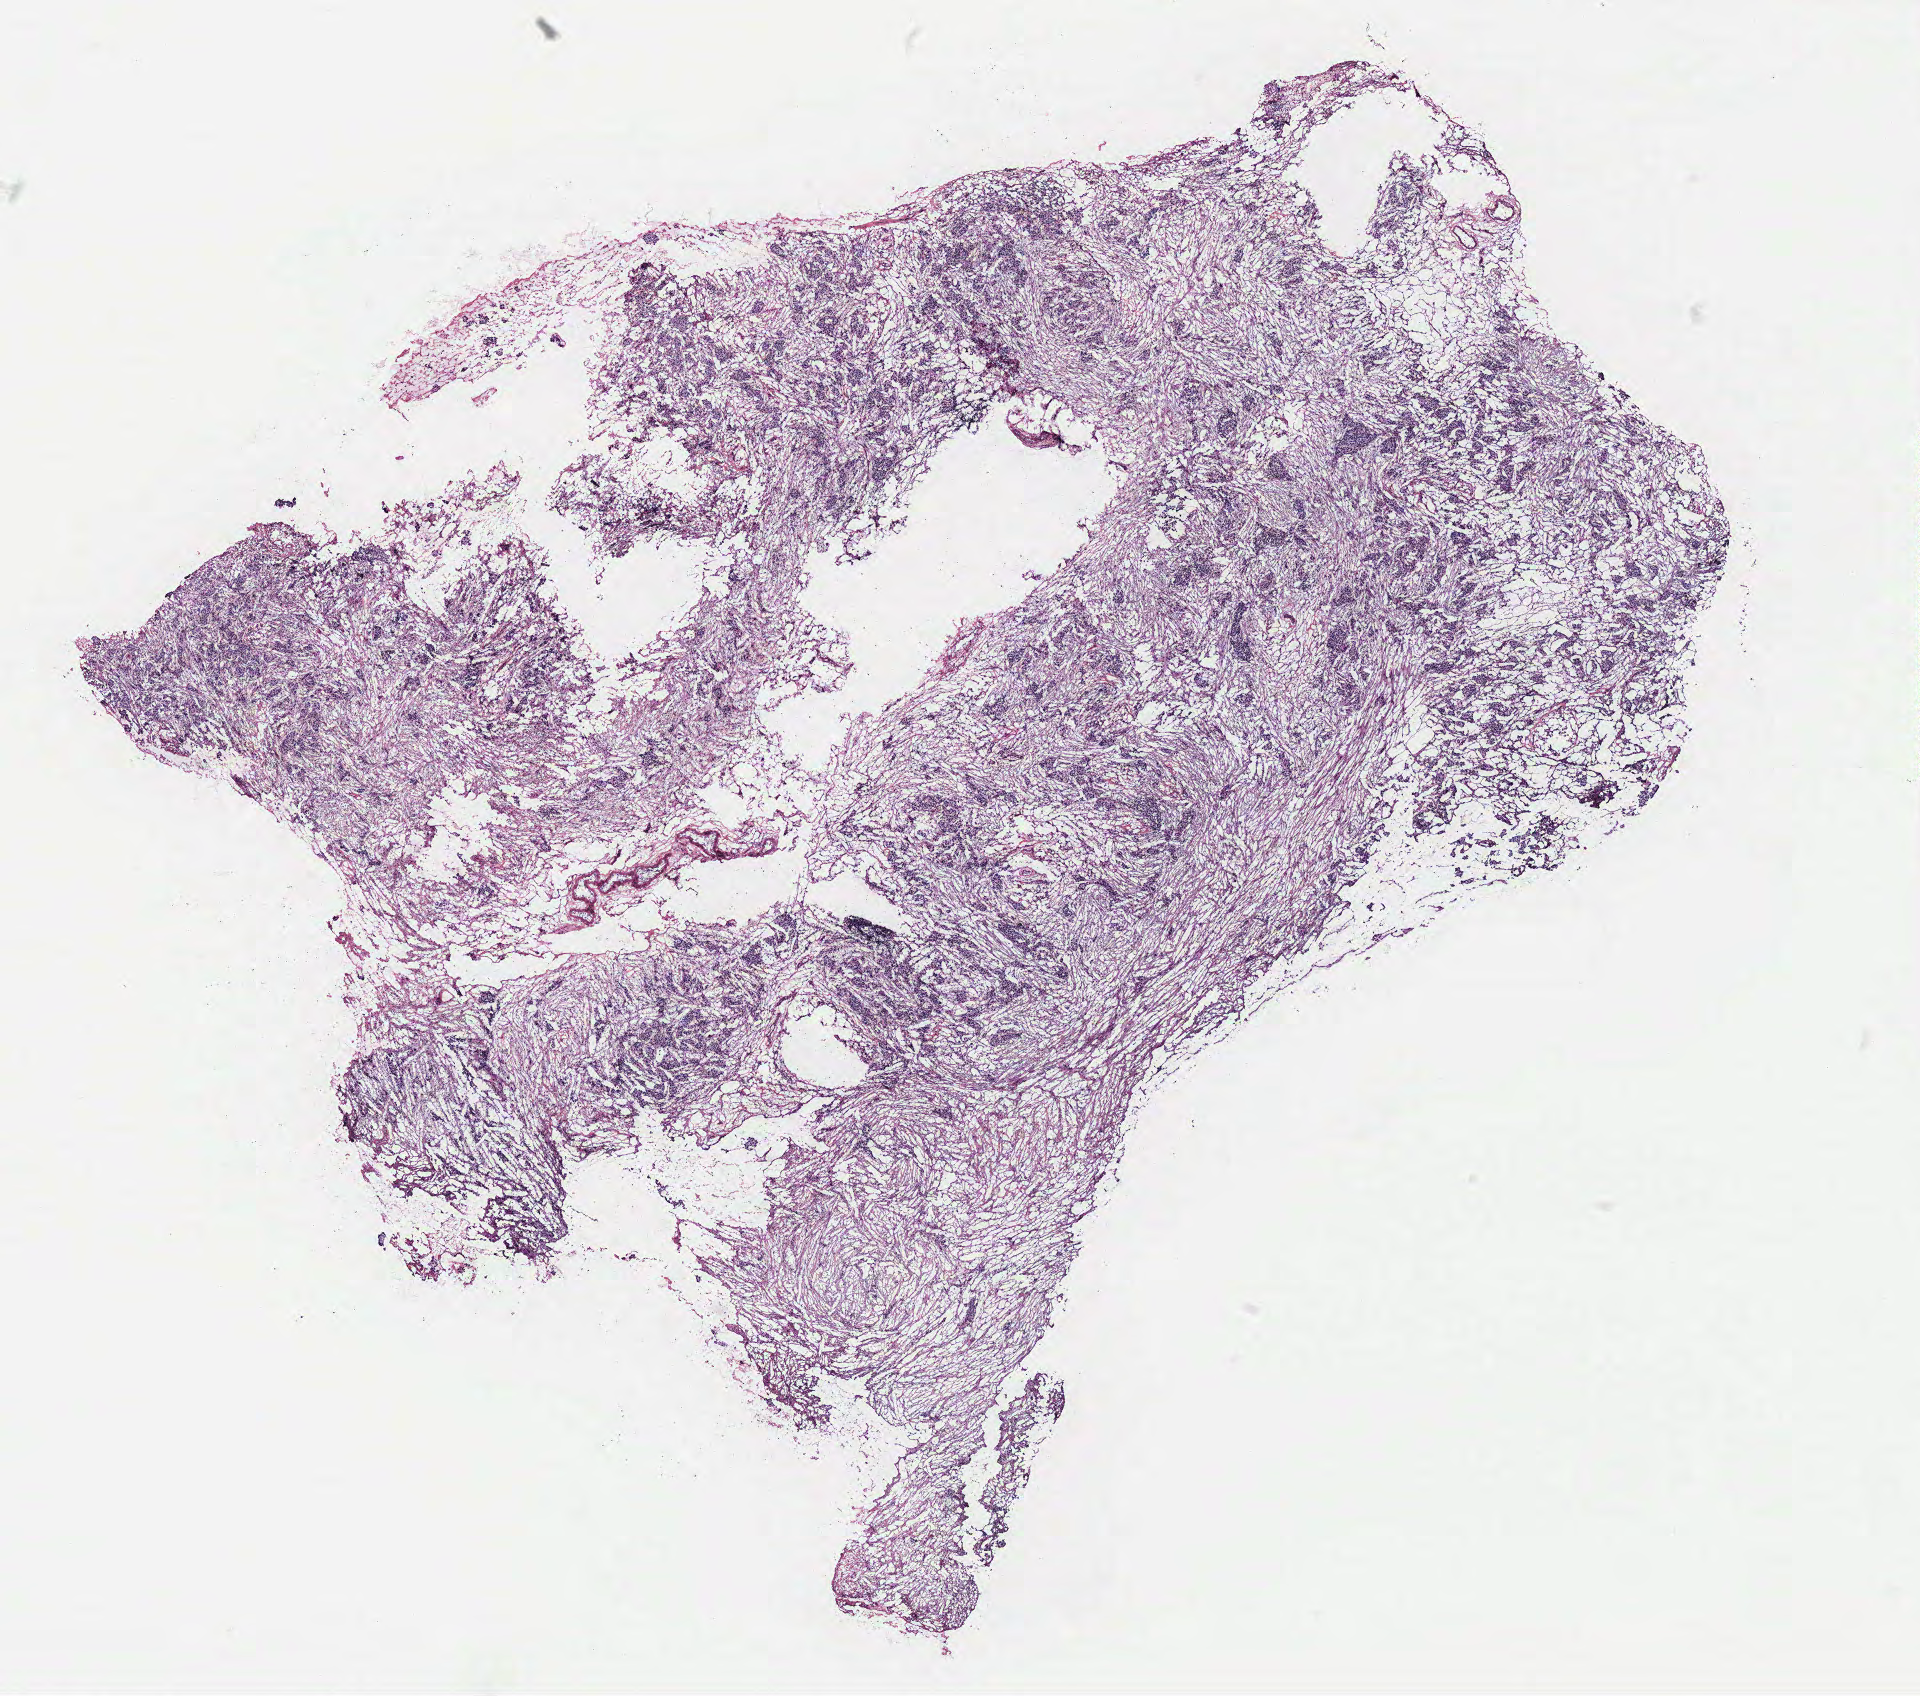
Digitized H&E-stained tissue section (whole slide), whole scanned area (about 15.4 x 13.6 mm, acquisition: 40x scan) shown as a low-resolution overview. Ovary, tumour tissue. Female, 58 y/o.
Primary tumour site (as recorded): fallopian tube. Histologic diagnosis: Serous adenocarcinoma, NOS (fallopian tube).